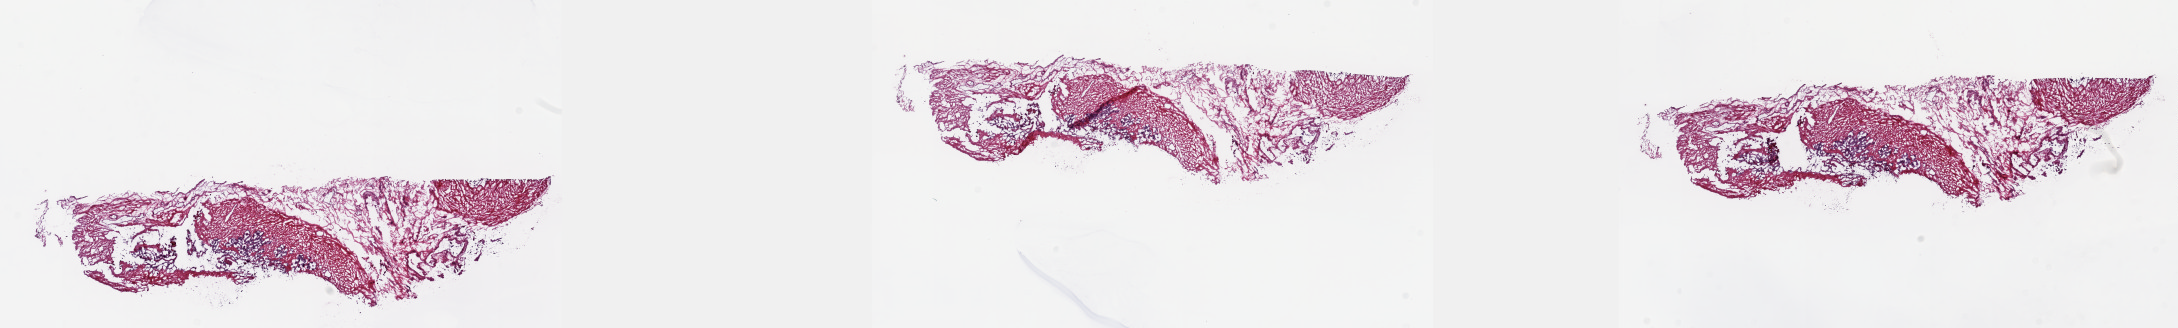
Digitized H&E-stained tissue section (whole slide) — a low-resolution overview of the entire scanned area, about 35.1 x 5.3 mm. Frozen section. Solid tissue normal (non-tumour tissue) sample from the prostate. Patient: male, age at initial diagnosis 50 years. Composition of this section per pathologist review: tumour cells 0%, tumour nuclei 0%, normal cells 15%, stromal cells 85%, necrosis 0%. Inflammatory infiltration, as recorded: lymphocyte infiltration 0%, monocyte infiltration 0%, neutrophil infiltration 0%.
This section: solid tissue normal (non-tumour) sample from the same patient. Patient diagnosis: Adenocarcinoma, NOS (prostate gland).